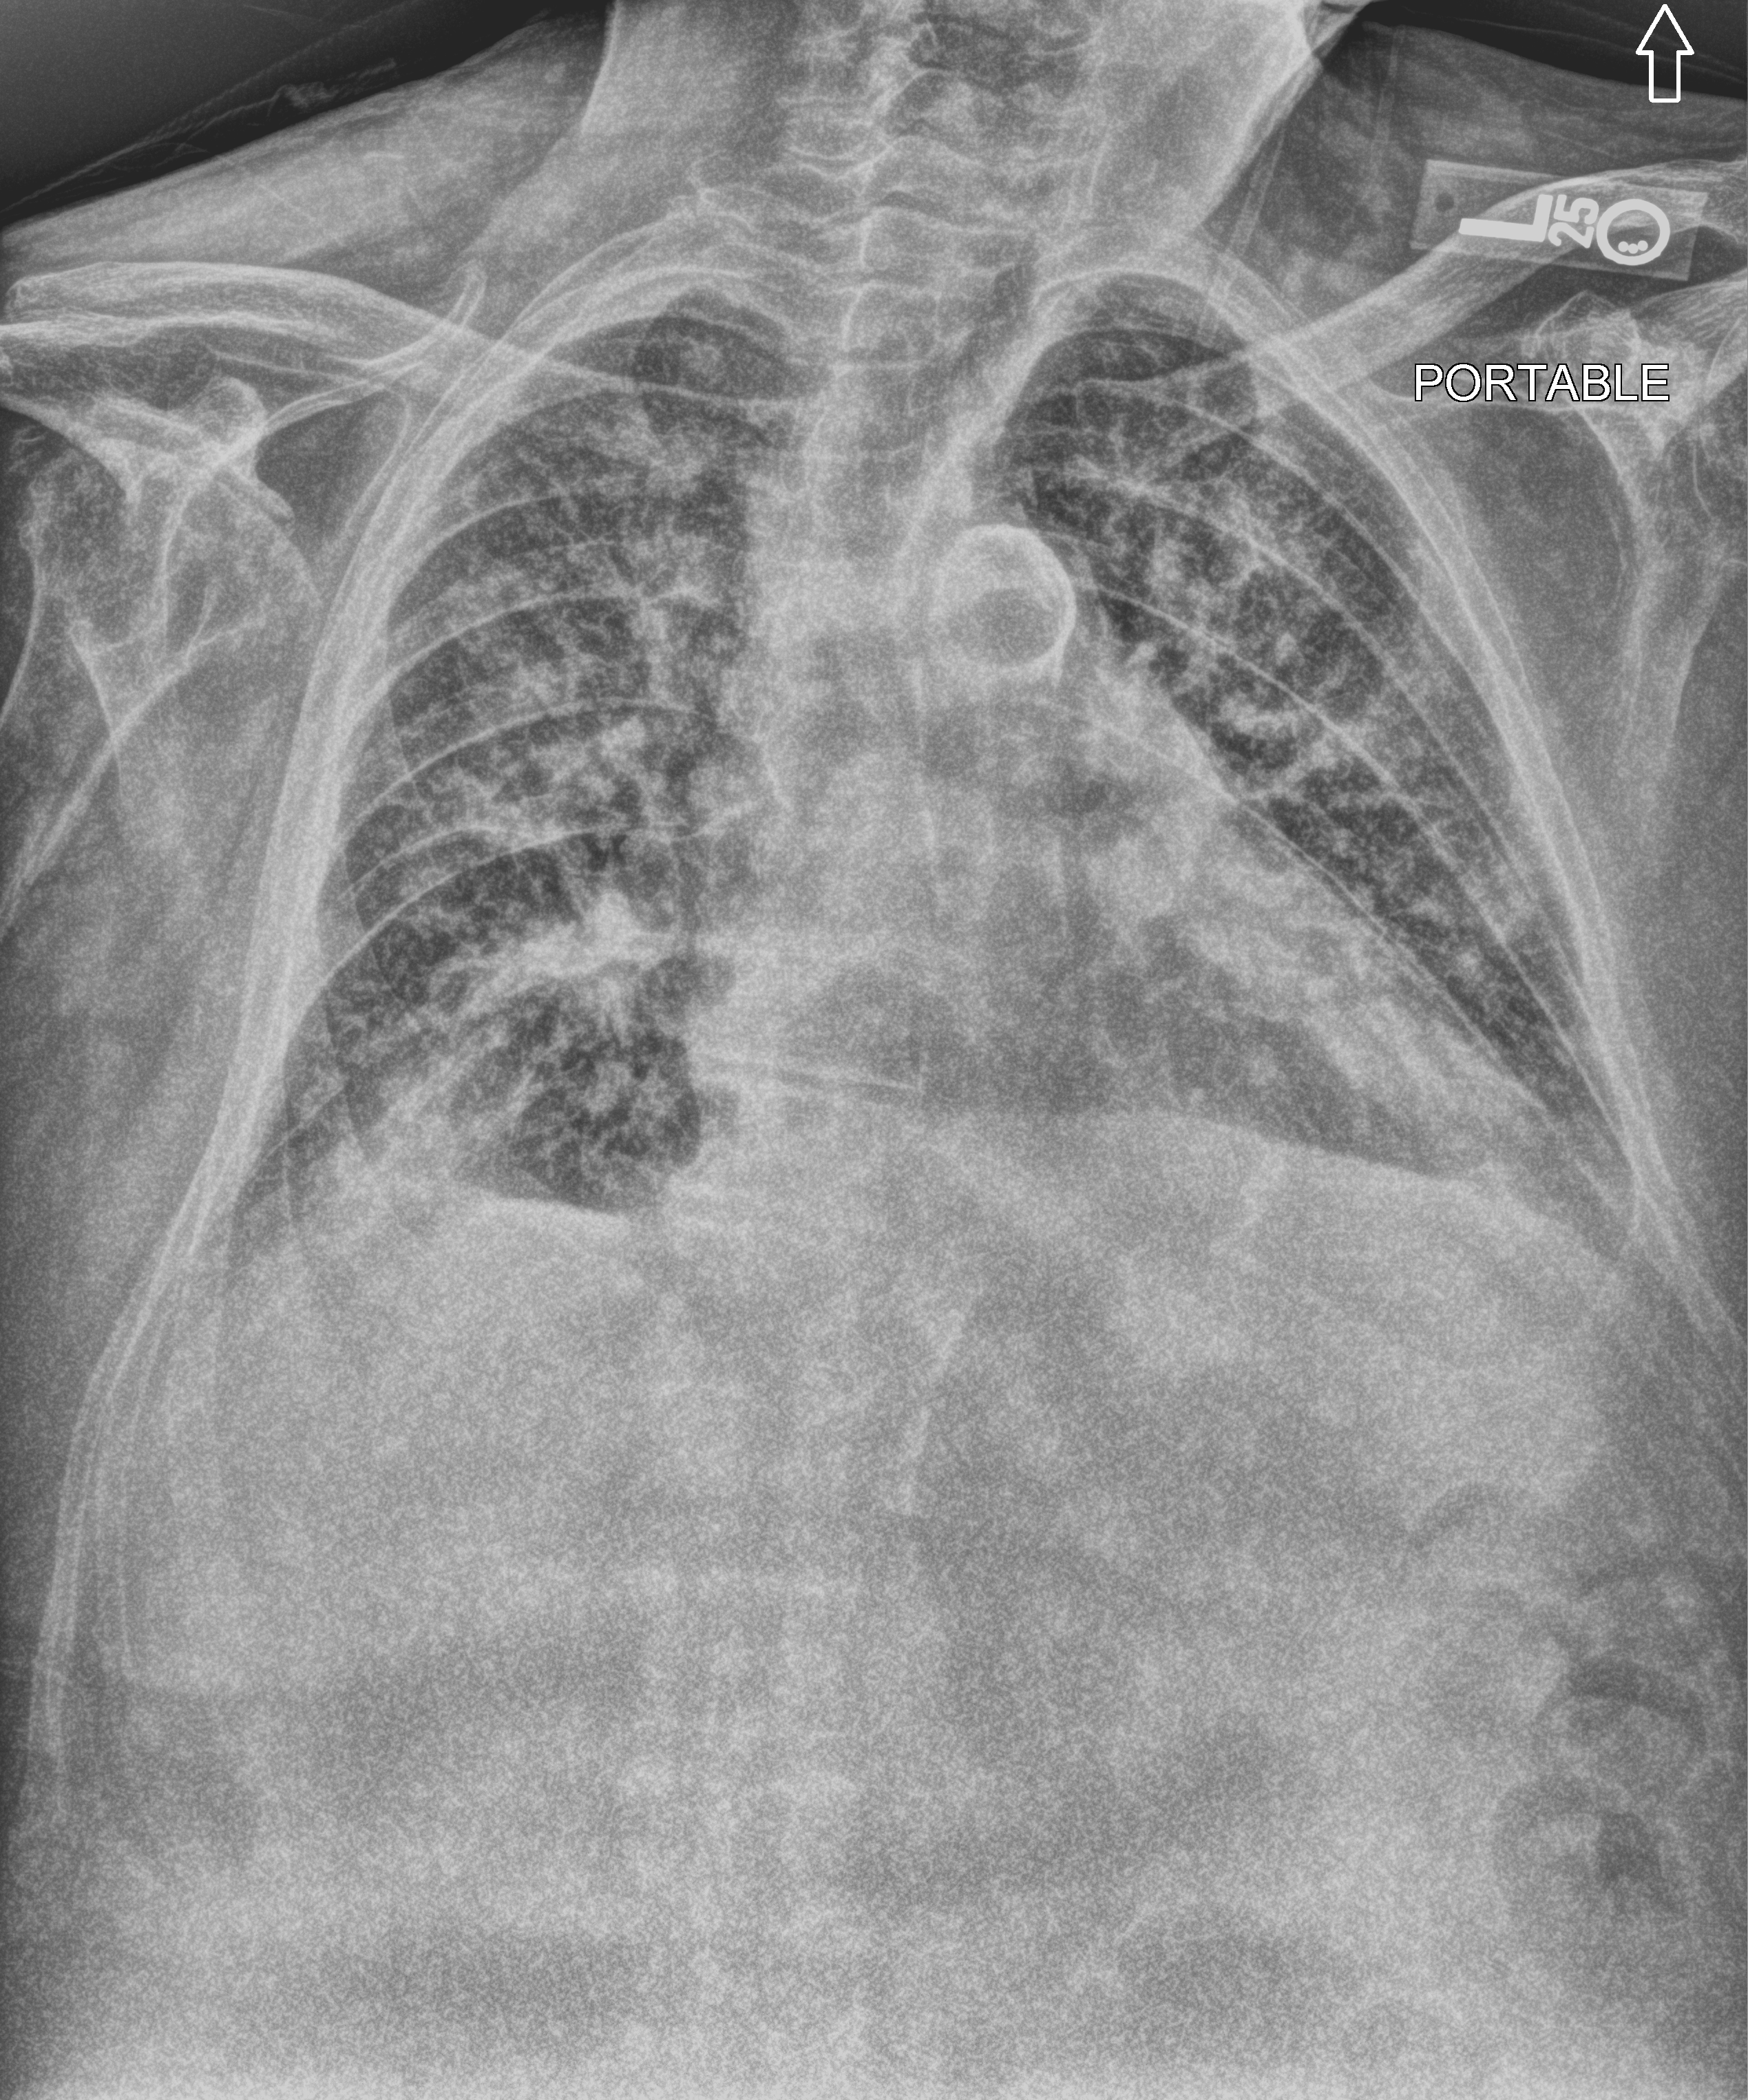
Chest X-ray (portable); anteroposterior (AP) projection. Patient hospitalised with COVID-19; male, aged 75–90 years.
From the hospital-stay record, not from the radiograph (when in the stay this image was taken is not recorded): chronic kidney disease (admission record): no.